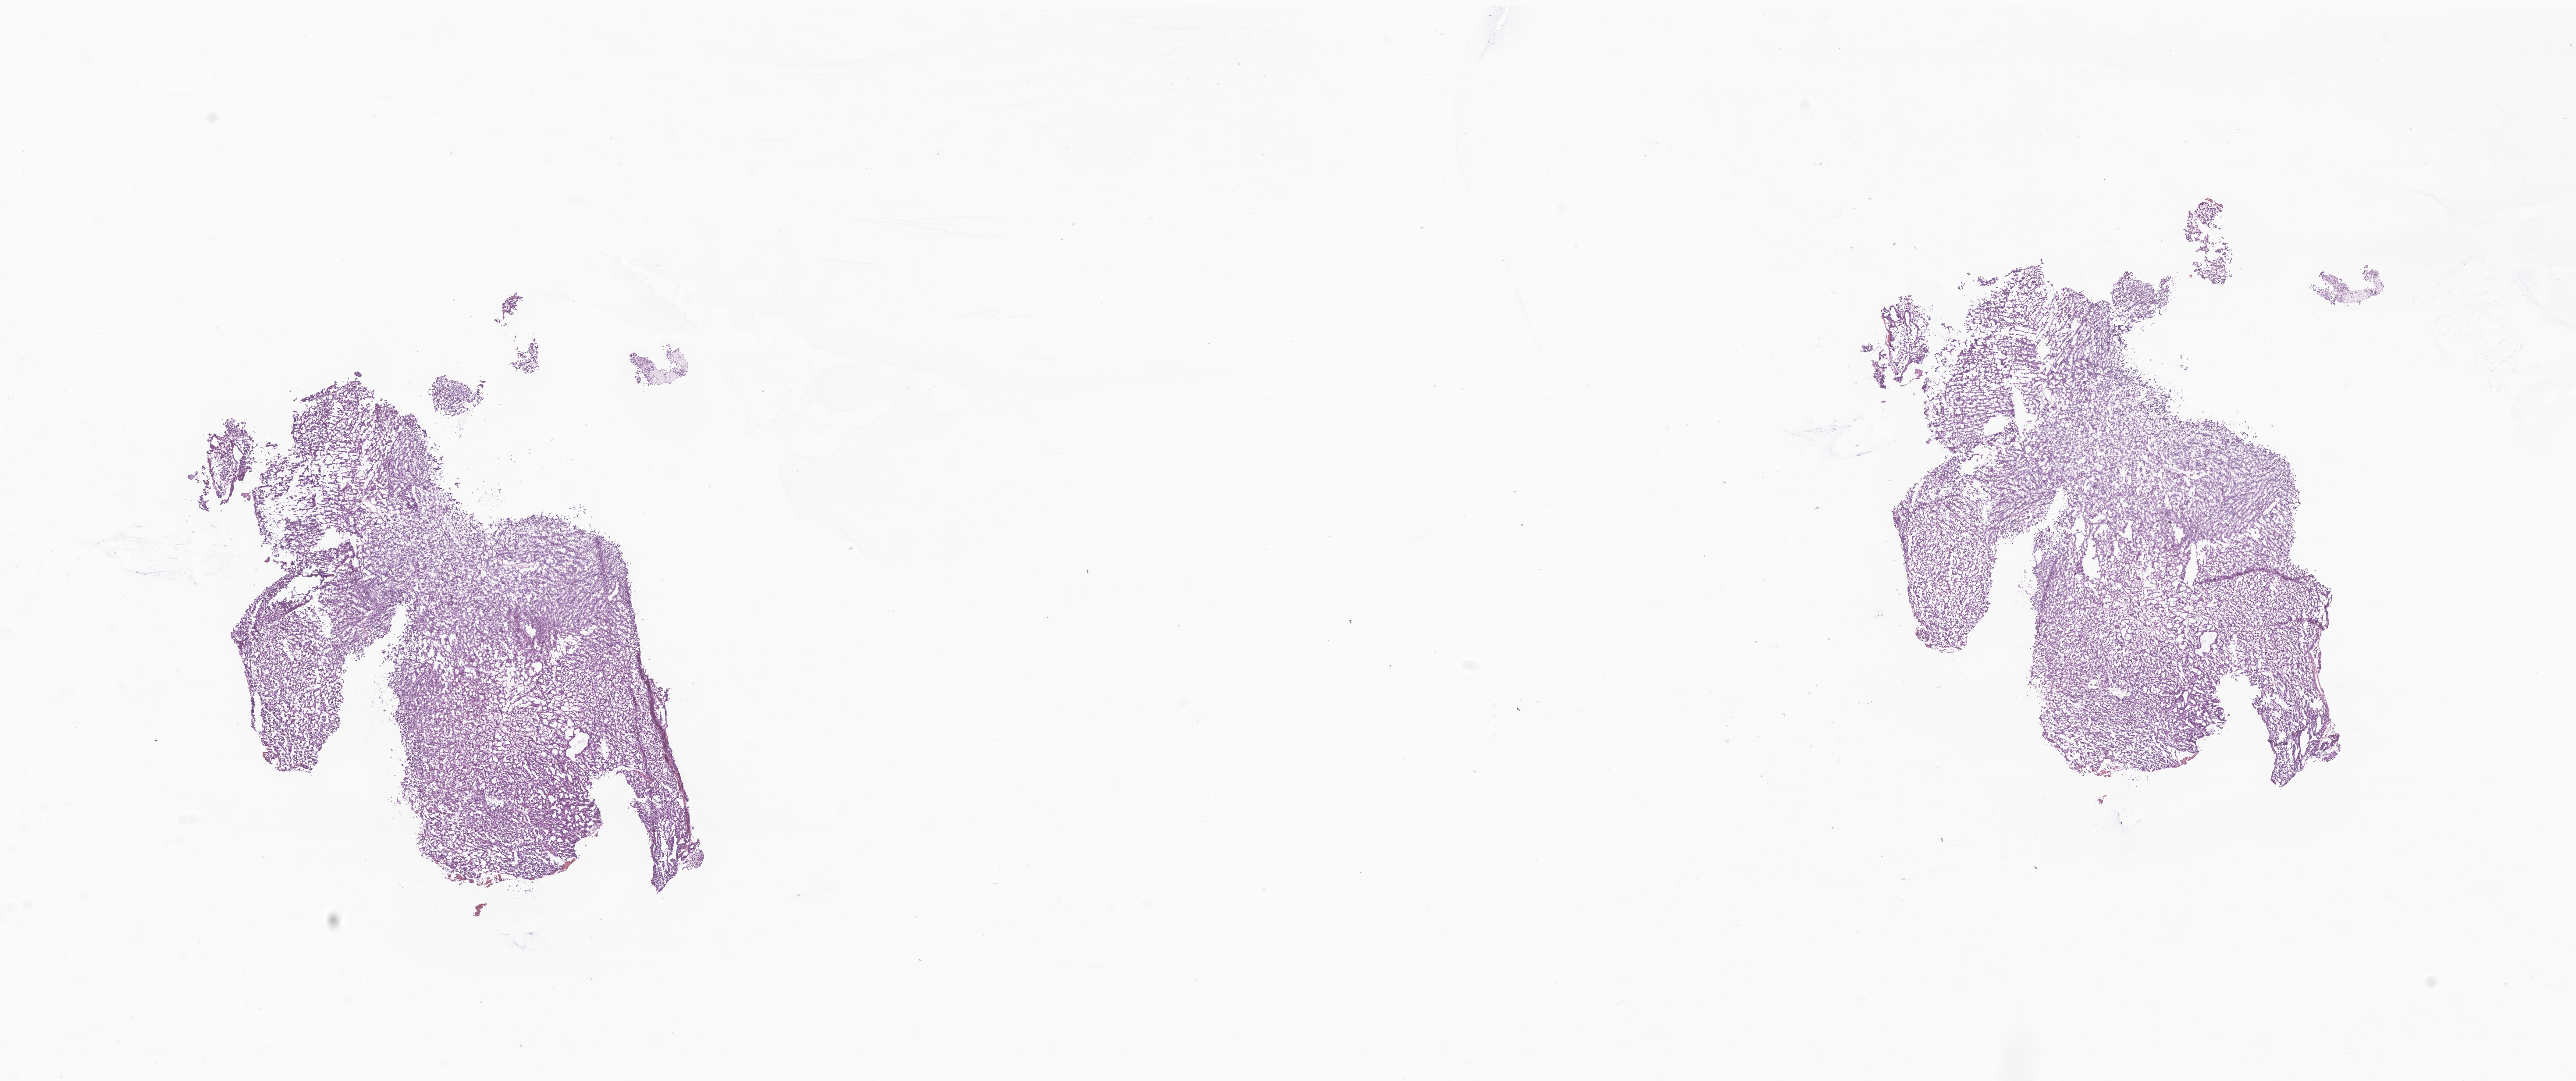
Whole-slide image, H&E stain of tumor tissue from the brain — shown as a low-resolution overview of the whole scanned area (about 24.8 x 10.4 mm); frozen section. Patient male; age 101 months (8 years 5 months).
- diagnosis: Neoplasm, malignant